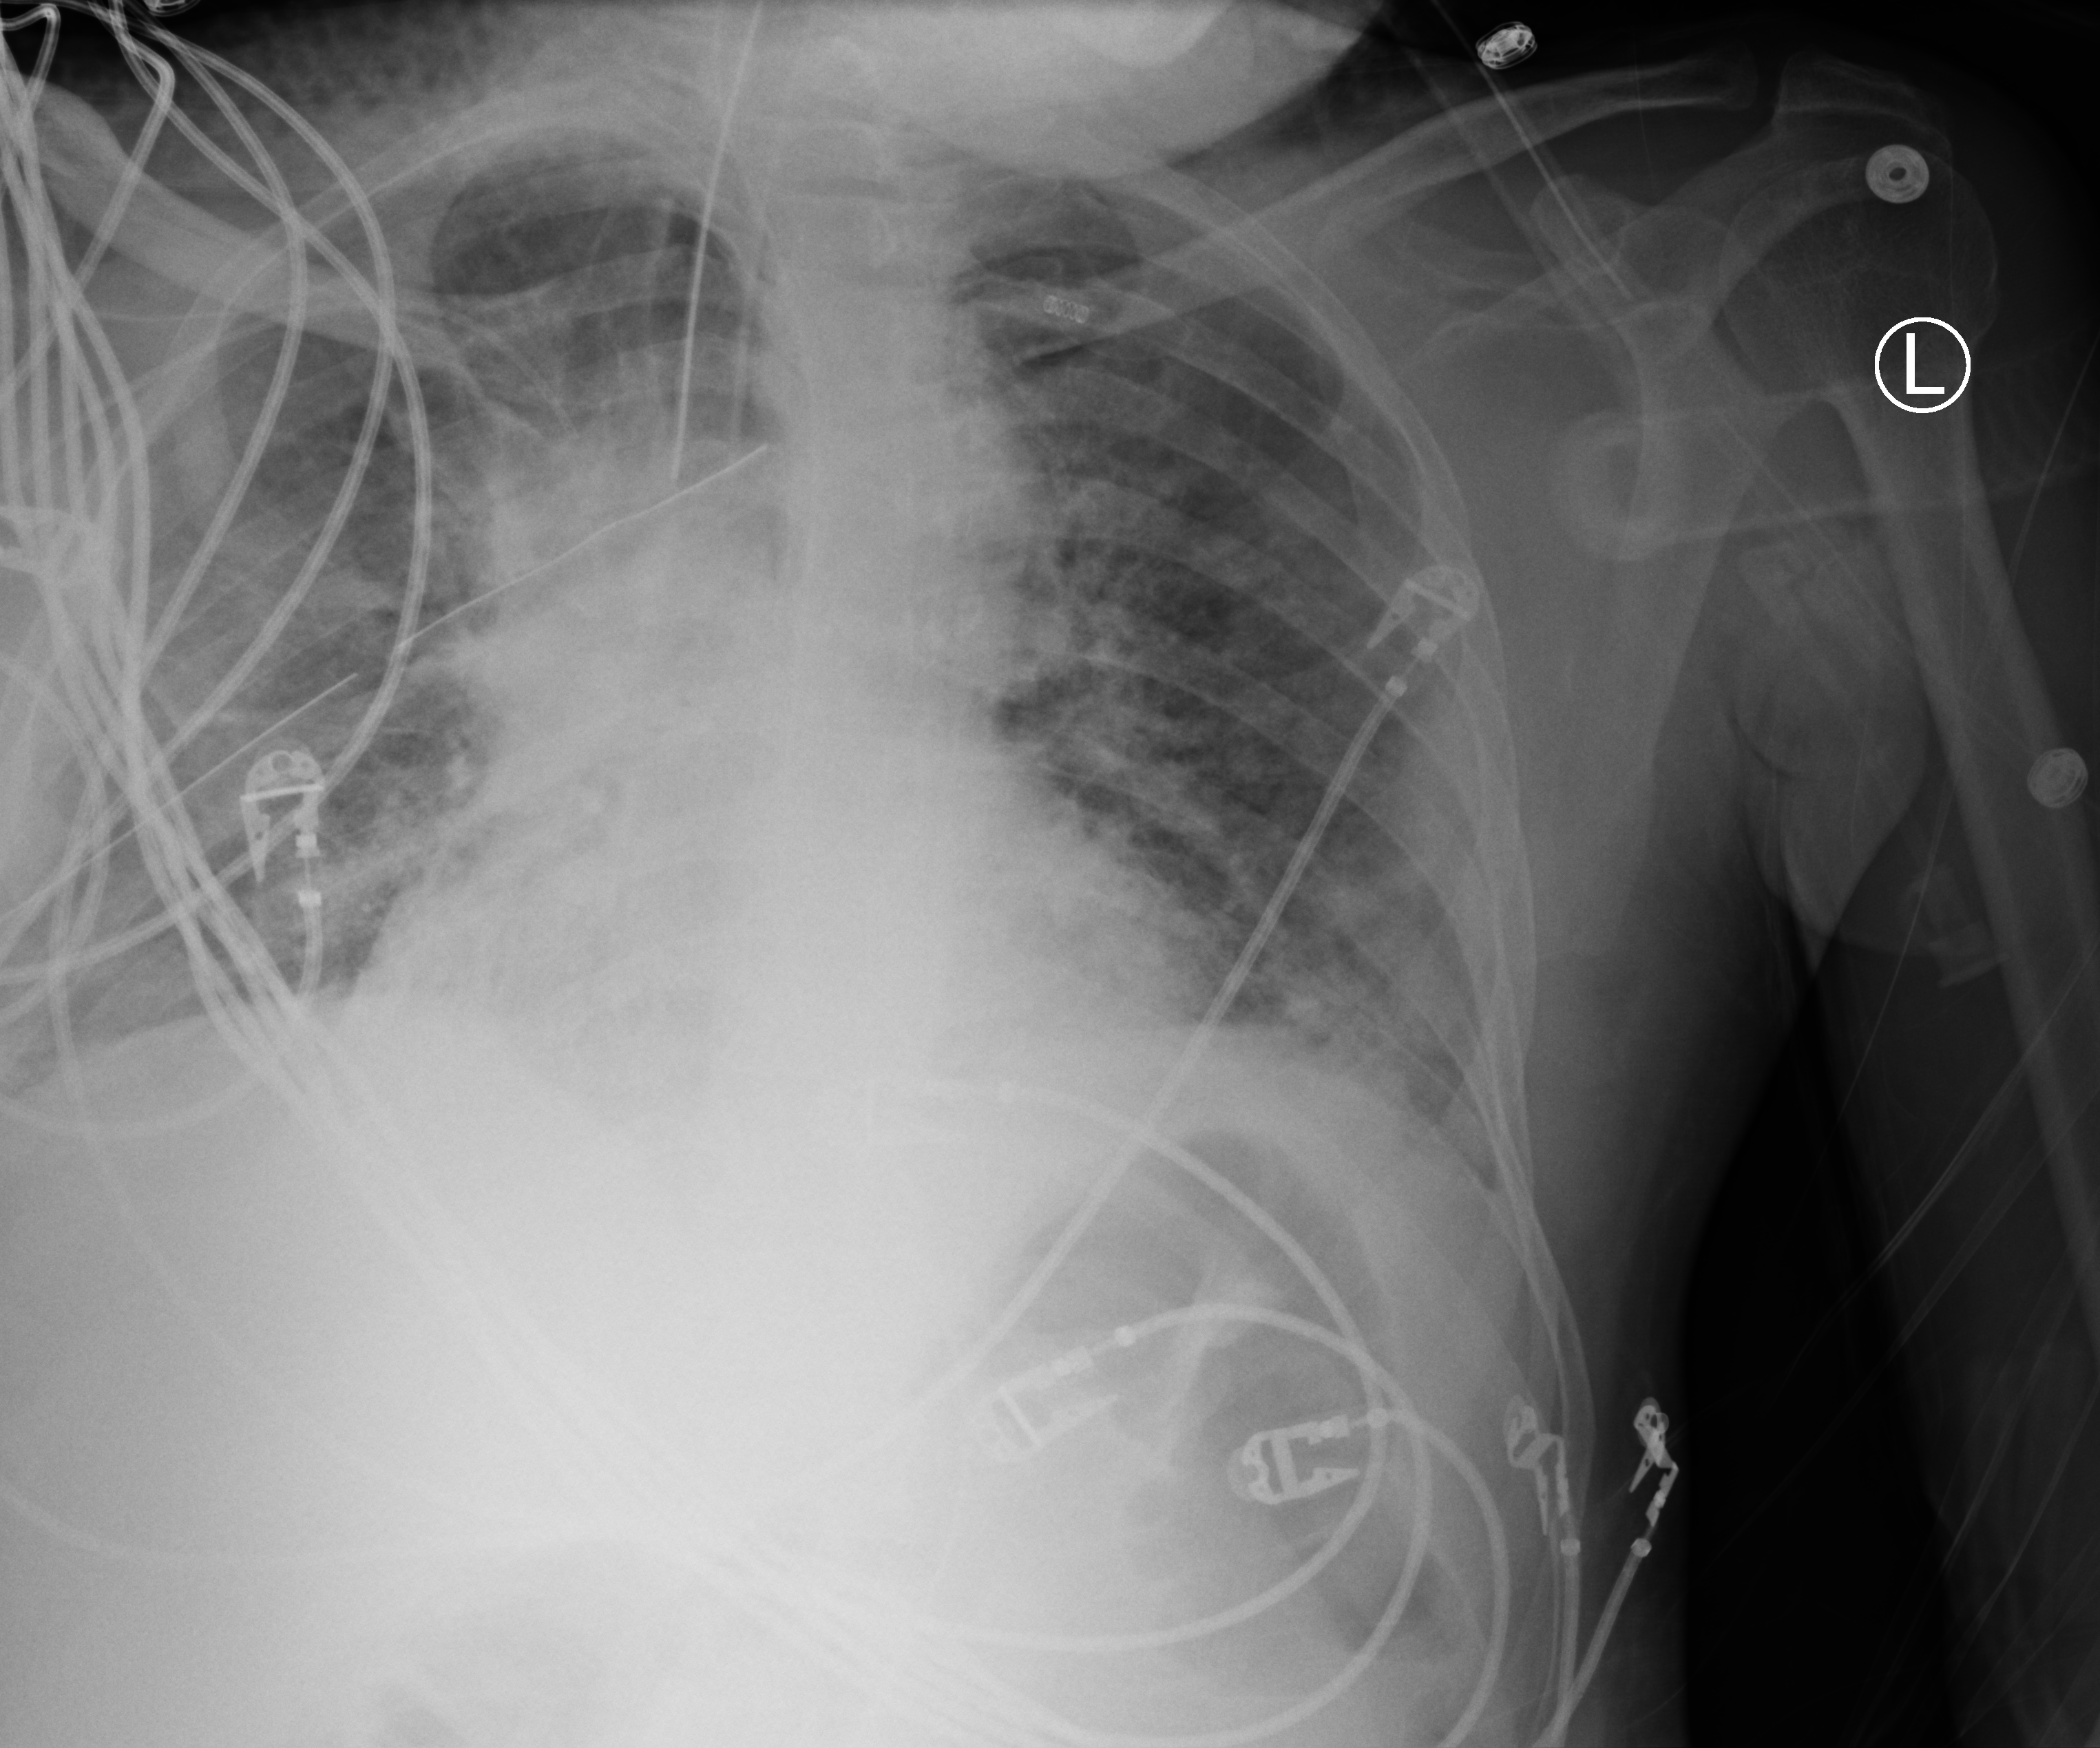
Bedside chest radiograph (computed radiography); anteroposterior (AP) projection. Patient hospitalised with COVID-19; male, aged 18–59 years.
Hospital-stay facts (about this admission, not read from this image; timing relative to this image not recorded): admitted to intensive care during this hospital stay: yes.